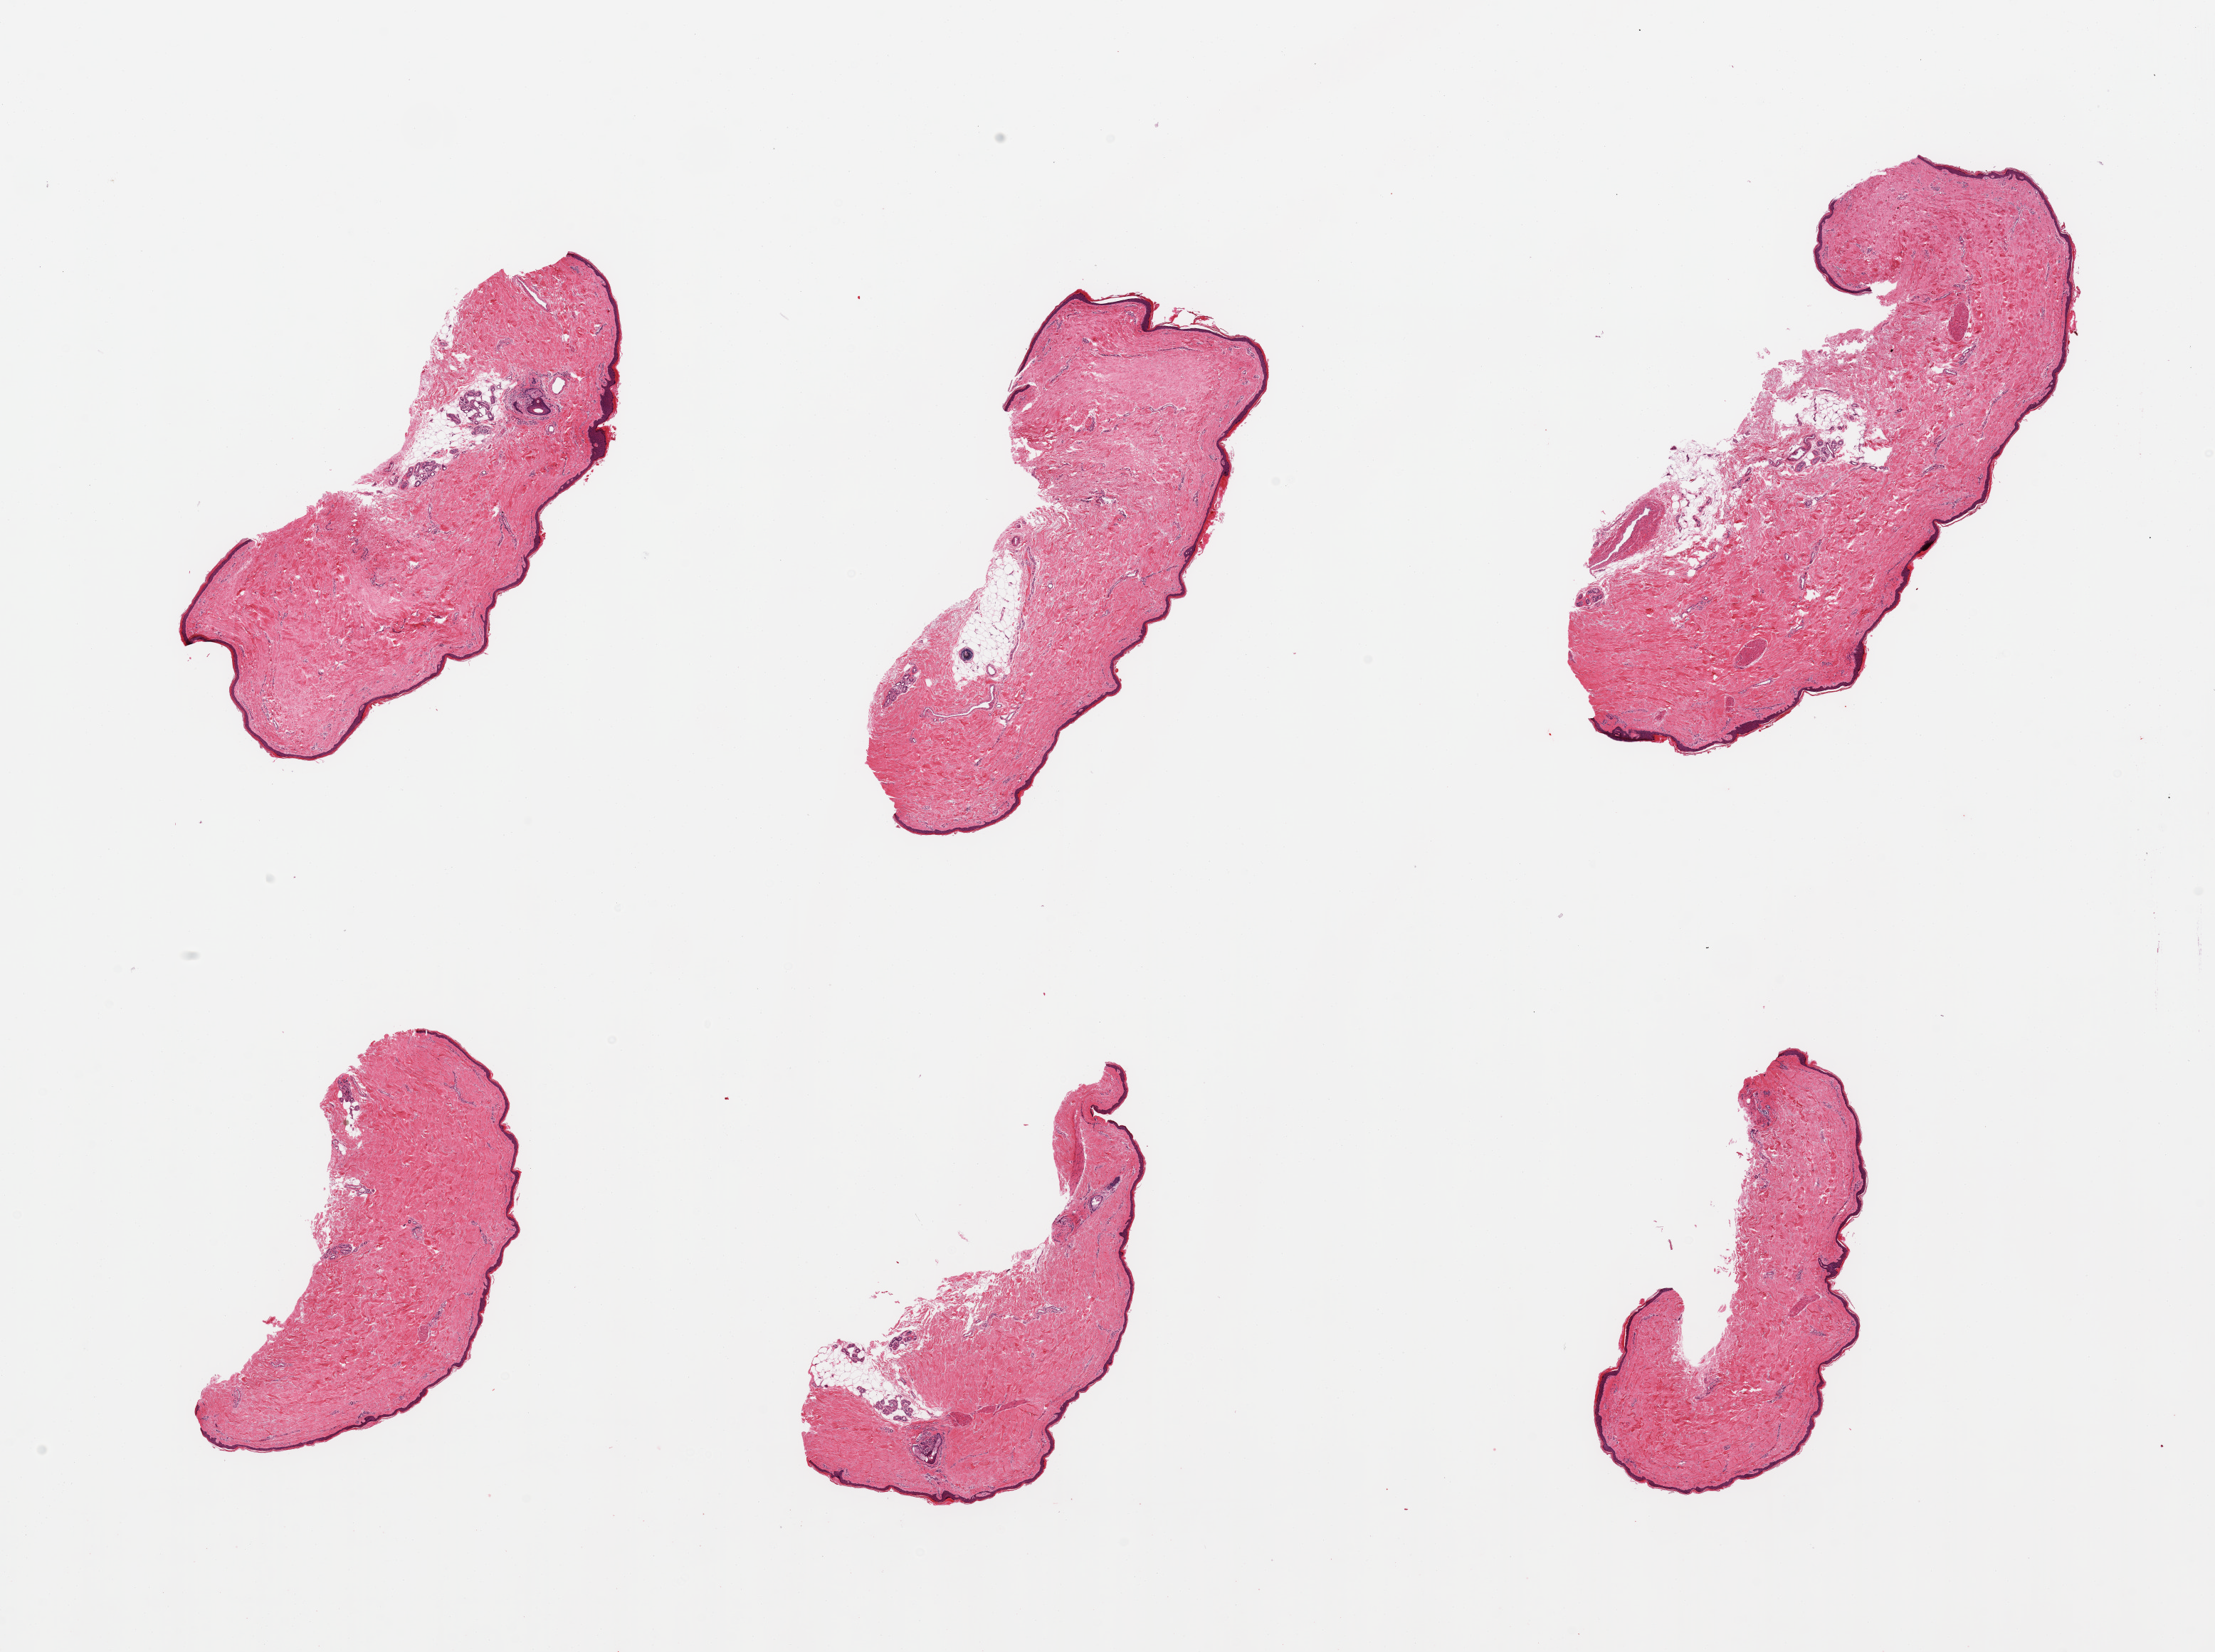
Digitized haematoxylin and eosin-stained section, brightfield — low-resolution overview of the scanned area, about 24.6 x 18.4 mm, PAXgene-fixed paraffin-embedded (PFPE) section, section of skin of lower leg (target tissue), donor tissue sample. Male donor.
Pathologist's review note for this sample: 6 pieces; up to 10% dermal fat; well trimmed.